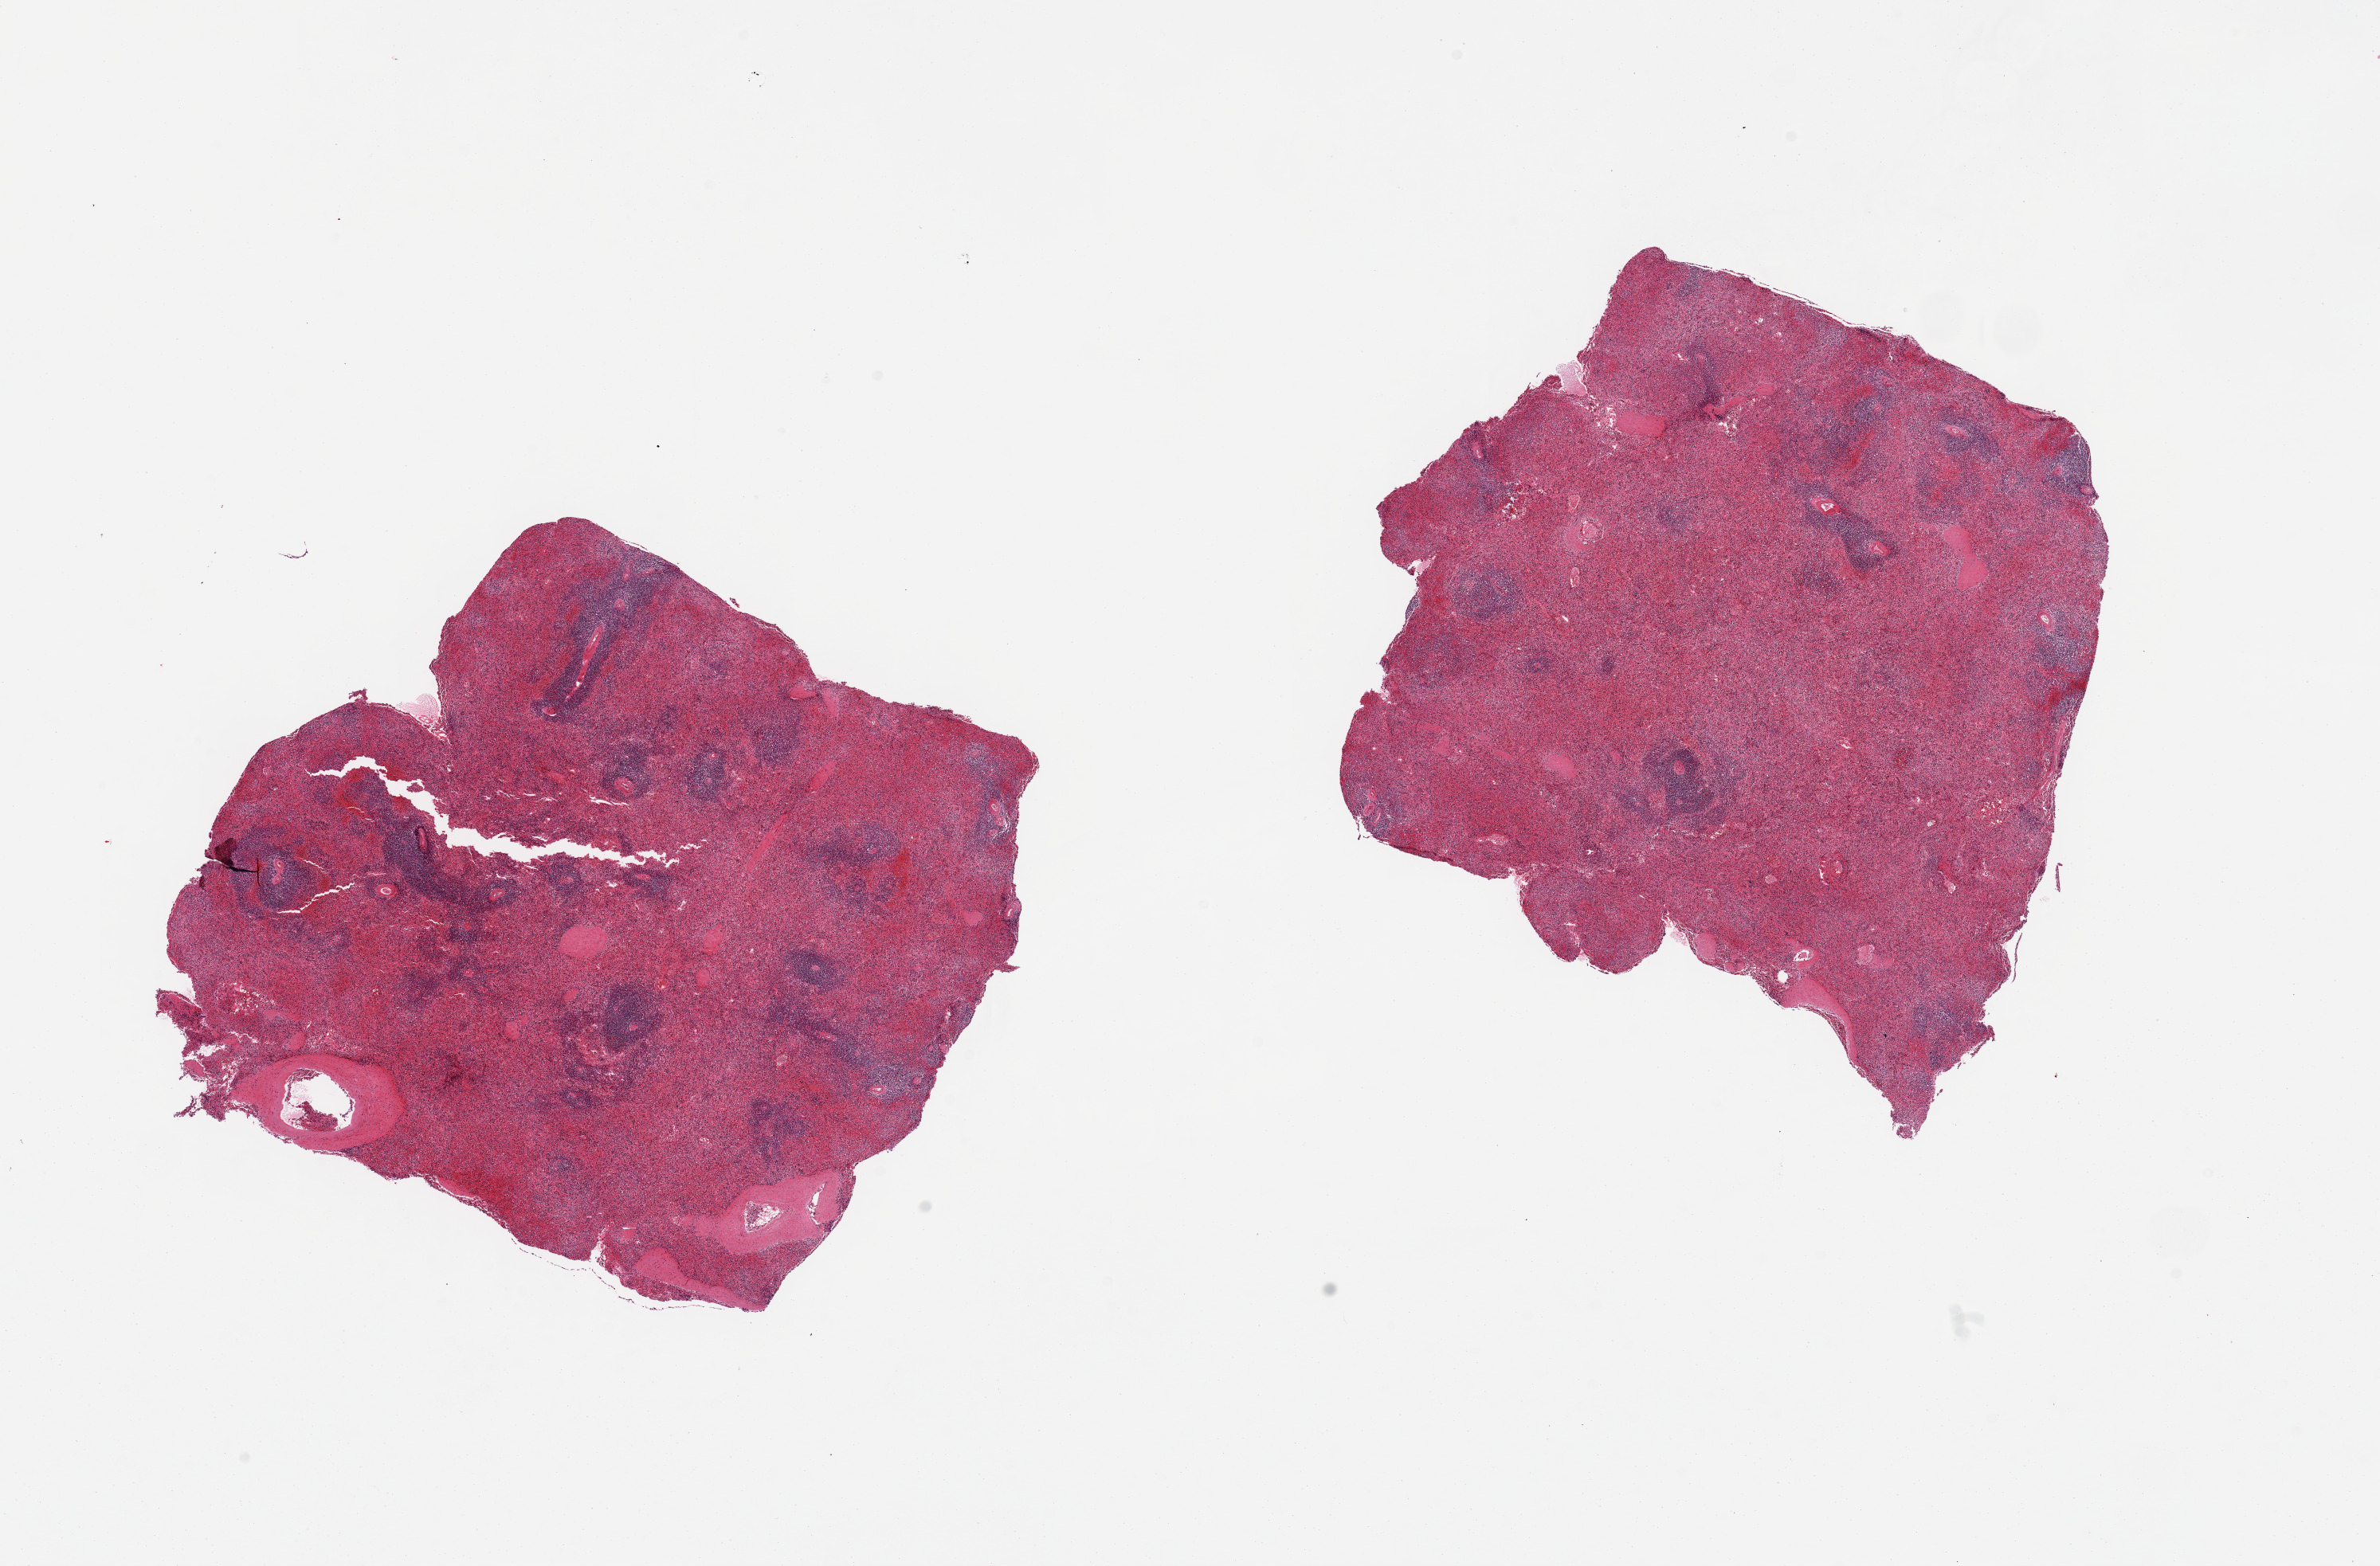
Whole-slide image, H&E stain, shown as a low-resolution overview of the whole scanned area (about 23.6 x 15.6 mm, from a 20x scan). PAXgene-fixed paraffin-embedded (PFPE) section. Target tissue: spleen. Donor tissue sample. Donor: female.
Reviewer comment on this tissue sample: 2 pieces; moderate congestion.